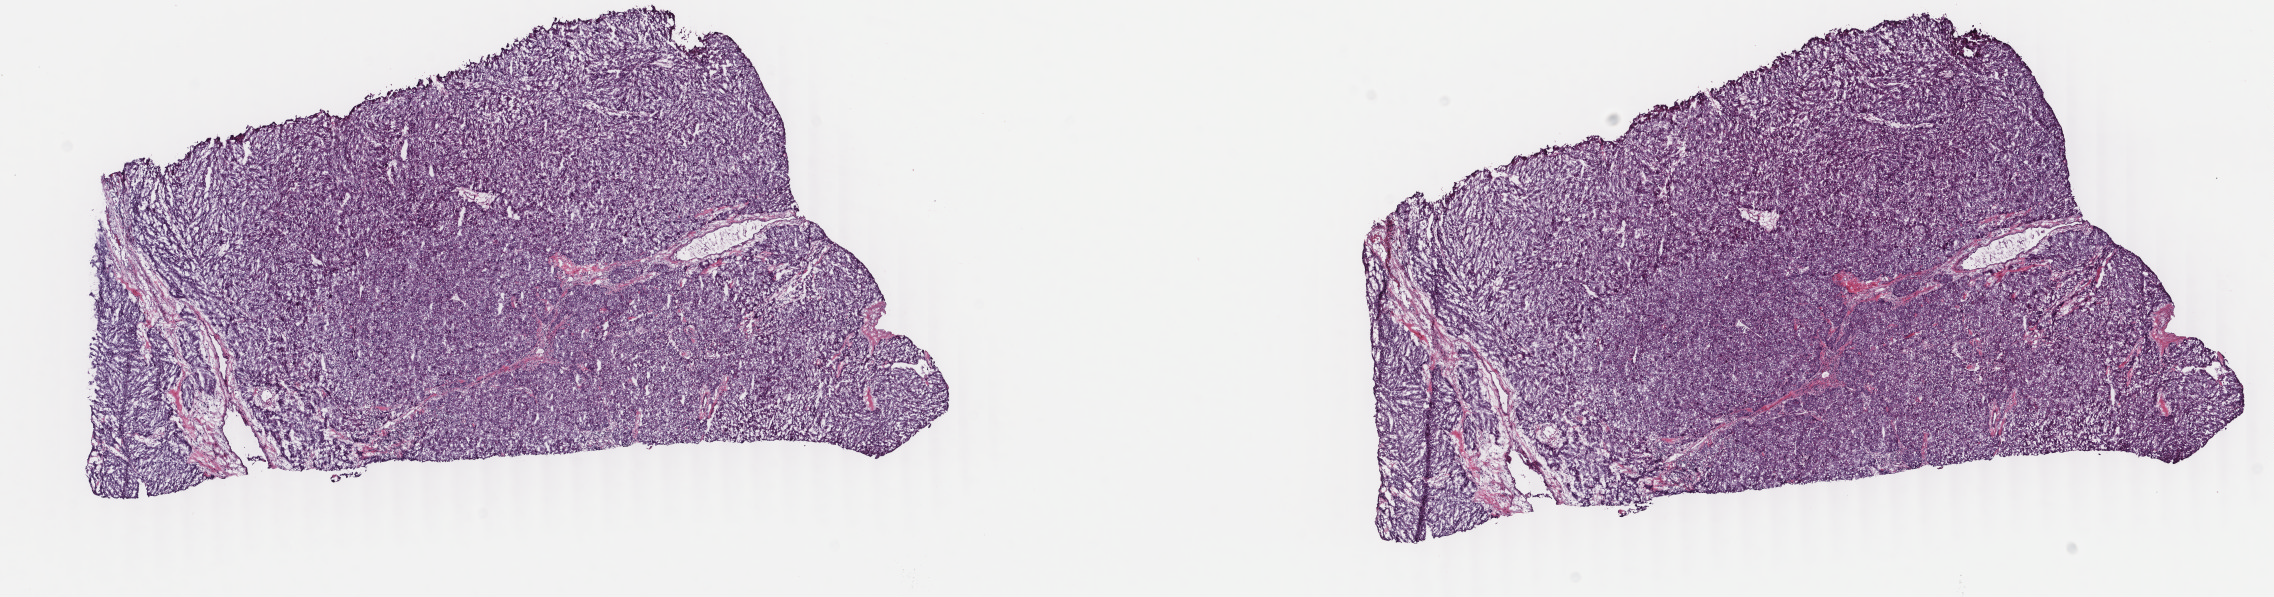
Whole-slide histology image, Hematoxylin and eosin (H&E) stained, a low-resolution overview of the entire scanned area, about 18.1 x 4.7 mm, frozen section from the top of the tissue portion, liver, primary tumour sample. Female, age 55 years at initial diagnosis. Histologic grade: G3 (poorly differentiated). Composition of this section per pathologist review: tumour cells 93%, tumour nuclei 93%, normal cells 0%, stromal cells 7%, necrosis 0%. Inflammatory infiltration, as recorded: lymphocyte infiltration 1%, monocyte infiltration 0%, neutrophil infiltration 0%.
Diagnosis: Hepatocellular carcinoma, NOS. AJCC pathologic stage: II (6th edition). TNM: T2 N0 M0.